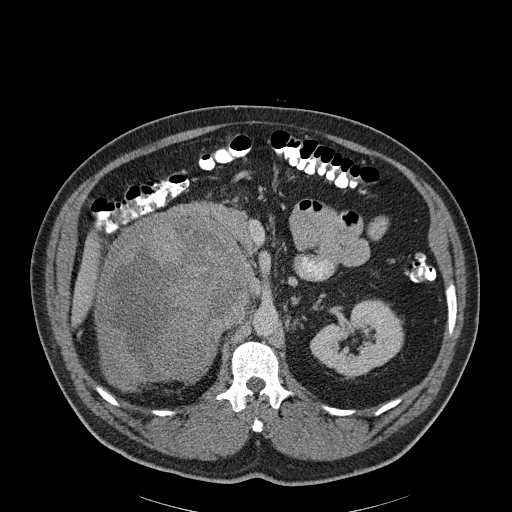
Contrast-enhanced abdominal CT, one axial slice; position 124 of 186 along the scan axis; reconstruction kernel B30f; 120 kVp; soft-tissue window (W 400 / L 40 HU); 3 mm slice thickness; 512 × 512 image matrix, field of view 464 × 464 mm. Male patient, age 56 years. From the clinical record (not read from this slice): diagnosis: adrenocortical carcinoma; tumour side: right adrenal; tumour size at pathology: 18 cm; Ki-67 index: 2 %; stage (as recorded): 3.
Annotated regions visible in this slice (semi-automatic segmentation, software-assisted and operator-edited):
- mass: box from (x=98, y=220) to (x=249, y=390) px